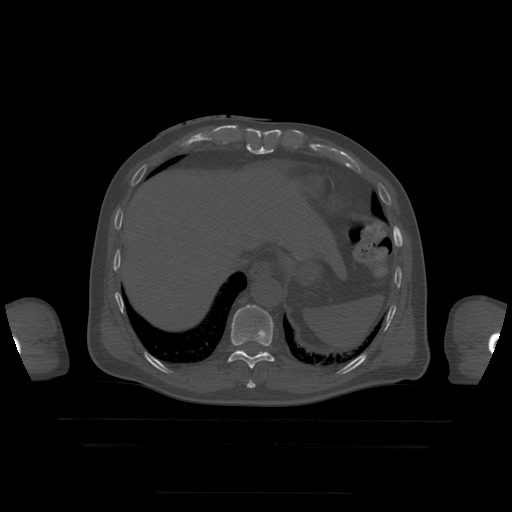
CT including the spine, one axial slice; slice 240 of 522 in the series (ordered by position); bone window (W 1800 / L 400 HU); 1.25 mm slice thickness; 512 × 512 image matrix. Patient age 68 years. From the clinical record (not read from this slice): primary cancer: urothelial.
Structures marked on this image (semi-automatic segmentation, software-assisted and operator-edited):
- T10 vertebra: bounding box <228,305,274,369> (left, top, right, bottom; pixels)
- T9 vertebra: <247,380,256,389>